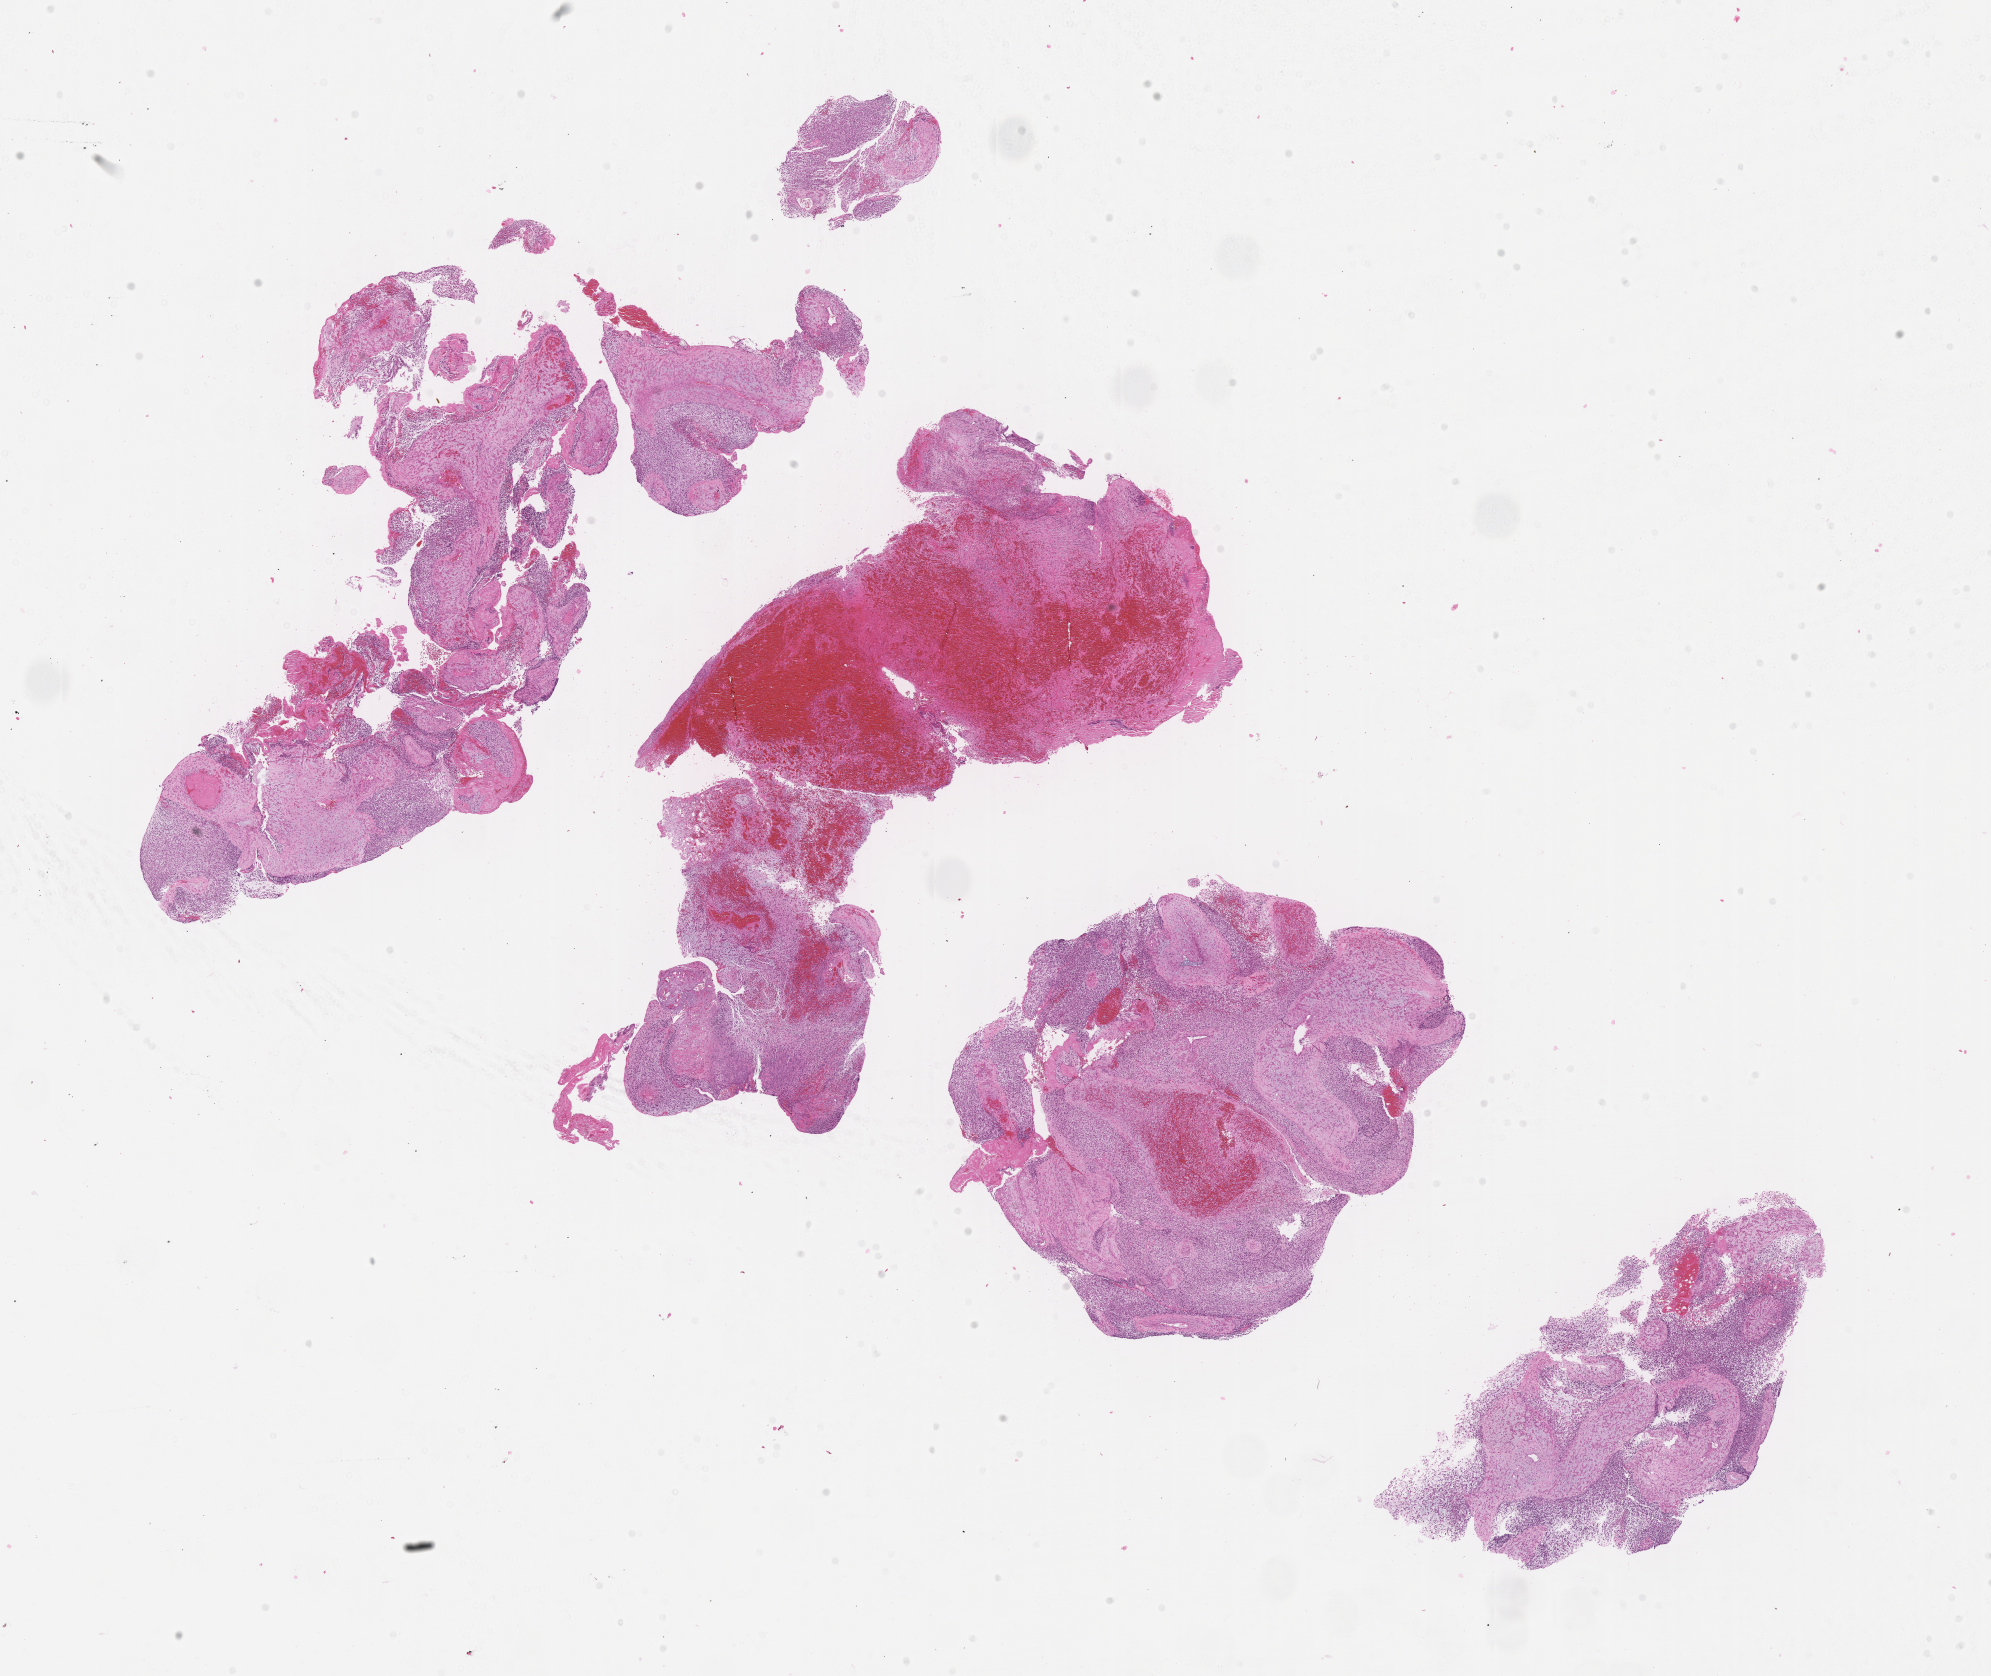
Digitized hematoxylin and eosin (H&E)-stained section of tumor tissue, low-resolution overview of the scanned area, about 16.1 x 13.6 mm, FFPE section, site: nasal cavity. Patient: male, age 6.5 years at diagnosis.
Metastatic status at presentation (as recorded): non-metastatic. Stage (as recorded): 2. Primary site (case record): nasopharynx. Diagnosis: rhabdomyosarcoma; histological classification: embryonal rhabdomyosarcoma.